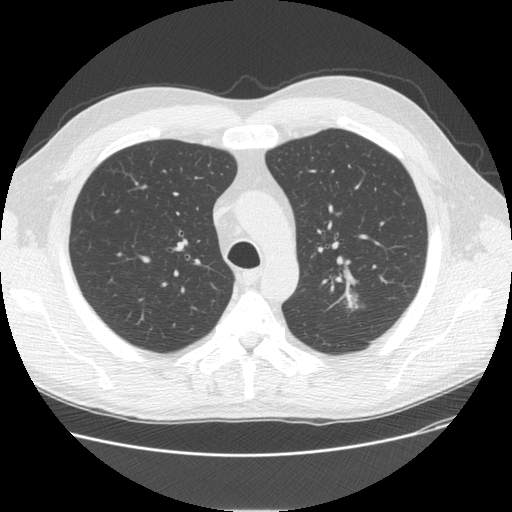
Low-dose screening chest CT, axial slice. Third screening round (two years after baseline). Lung window (W 1500 / L -600 HU). 2.5 mm slice thickness. Male participant, aged 57 years at enrolment.
- Lesion marked by an expert reader, bounding box [x1, y1, x2, y2] px = [322, 283, 375, 321].
- Screening reader's record for this exam (one nodule recorded; not confirmed to be the boxed lesion): non-calcified nodule or mass ≥4 mm, left upper lobe, 17 × 13 mm, spiculated (stellate) margins, mixed attenuation, pre-existing on the prior screen: yes; interval growth: yes.